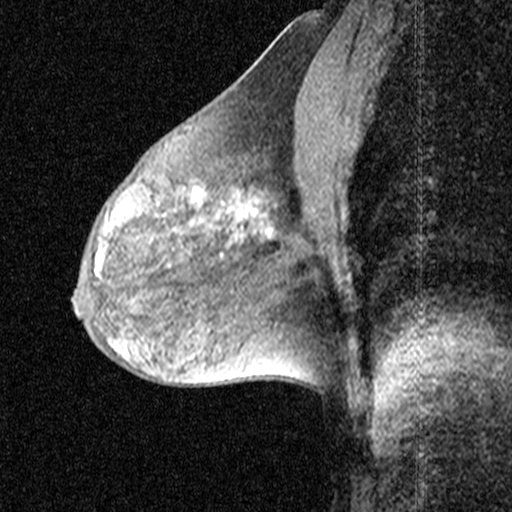
Breast MRI (dynamic contrast-enhanced), one sagittal slice. Slice 26 of 44 in the series (ordered by position). Dynamic contrast-enhanced study with each time point stored as its own series, time point 2 of 3 at this slice position (early post-contrast, ordered by acquisition time). 1.5 T. TE 4.5 ms, TR 11 ms. 3 mm slice thickness. 512 × 512 image matrix, field of view 200 × 200 mm. Female patient, age 53 years. From the clinical record (not read from this slice): setting: breast cancer imaged before/during neoadjuvant chemotherapy; receptor status: HR-positive, HER2-negative.
Structures marked on this image (semi-automatically segmented with operator editing):
- analysis volume of interest (the breast-tissue region the enhancement analysis was run in; not a lesion): bounding box <198,152,299,267> (left, top, right, bottom; pixels)
- tumour enhancement mask (voxels above the 90 % enhancement threshold inside the analysis volume of interest): <231,201,257,211>